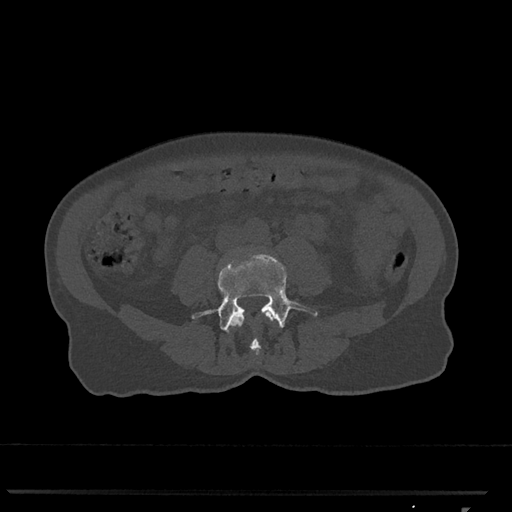
CT including the spine, one axial slice; slice 227 of 793 in the series (ordered by position); reconstruction kernel Br40s/3; bone window (W 1800 / L 400 HU); 512 × 512 image matrix, field of view 380 × 380 mm. Patient: female, 62 years. From the clinical record (not read from this slice): primary cancer: renal.
Annotated regions visible in this slice (semi-automatic segmentation, software-assisted and operator-edited):
- L3 vertebra: box from (x=230, y=312) to (x=275, y=355) px
- L4 vertebra: (x=192, y=255)–(x=318, y=333)